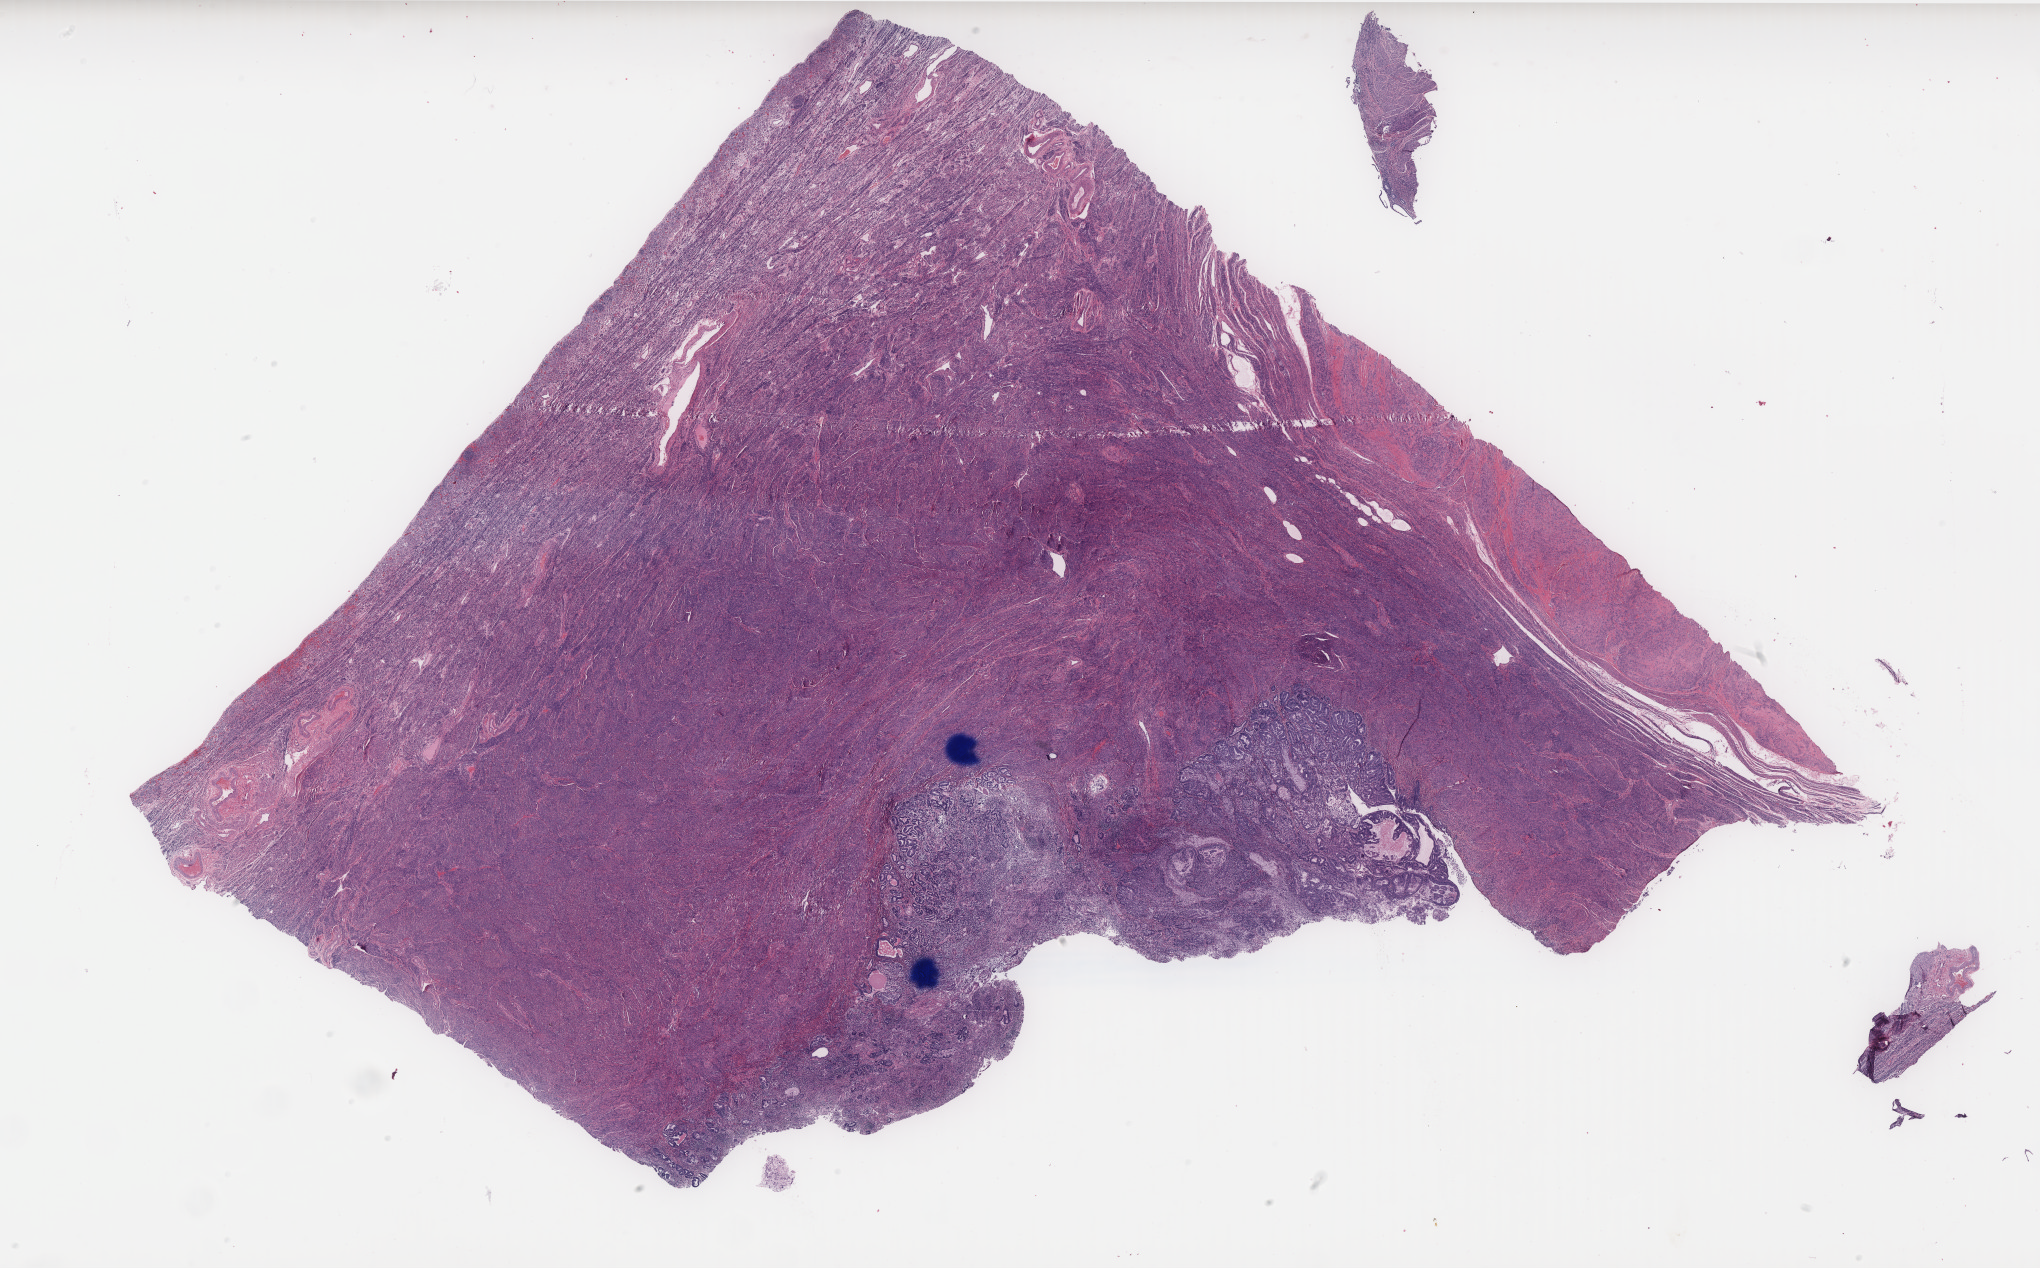
H&E-stained whole-slide image — a low-resolution overview of the entire scanned area, about 32.7 x 20.3 mm. Formalin-fixed paraffin-embedded (FFPE) diagnostic section. Uterus, primary tumour sample. Female patient; age at initial diagnosis 71 years. Histologic grade: G1 (well differentiated).
* FIGO stage: IA
* histologic diagnosis: Endometrioid adenocarcinoma, NOS (endometrium)